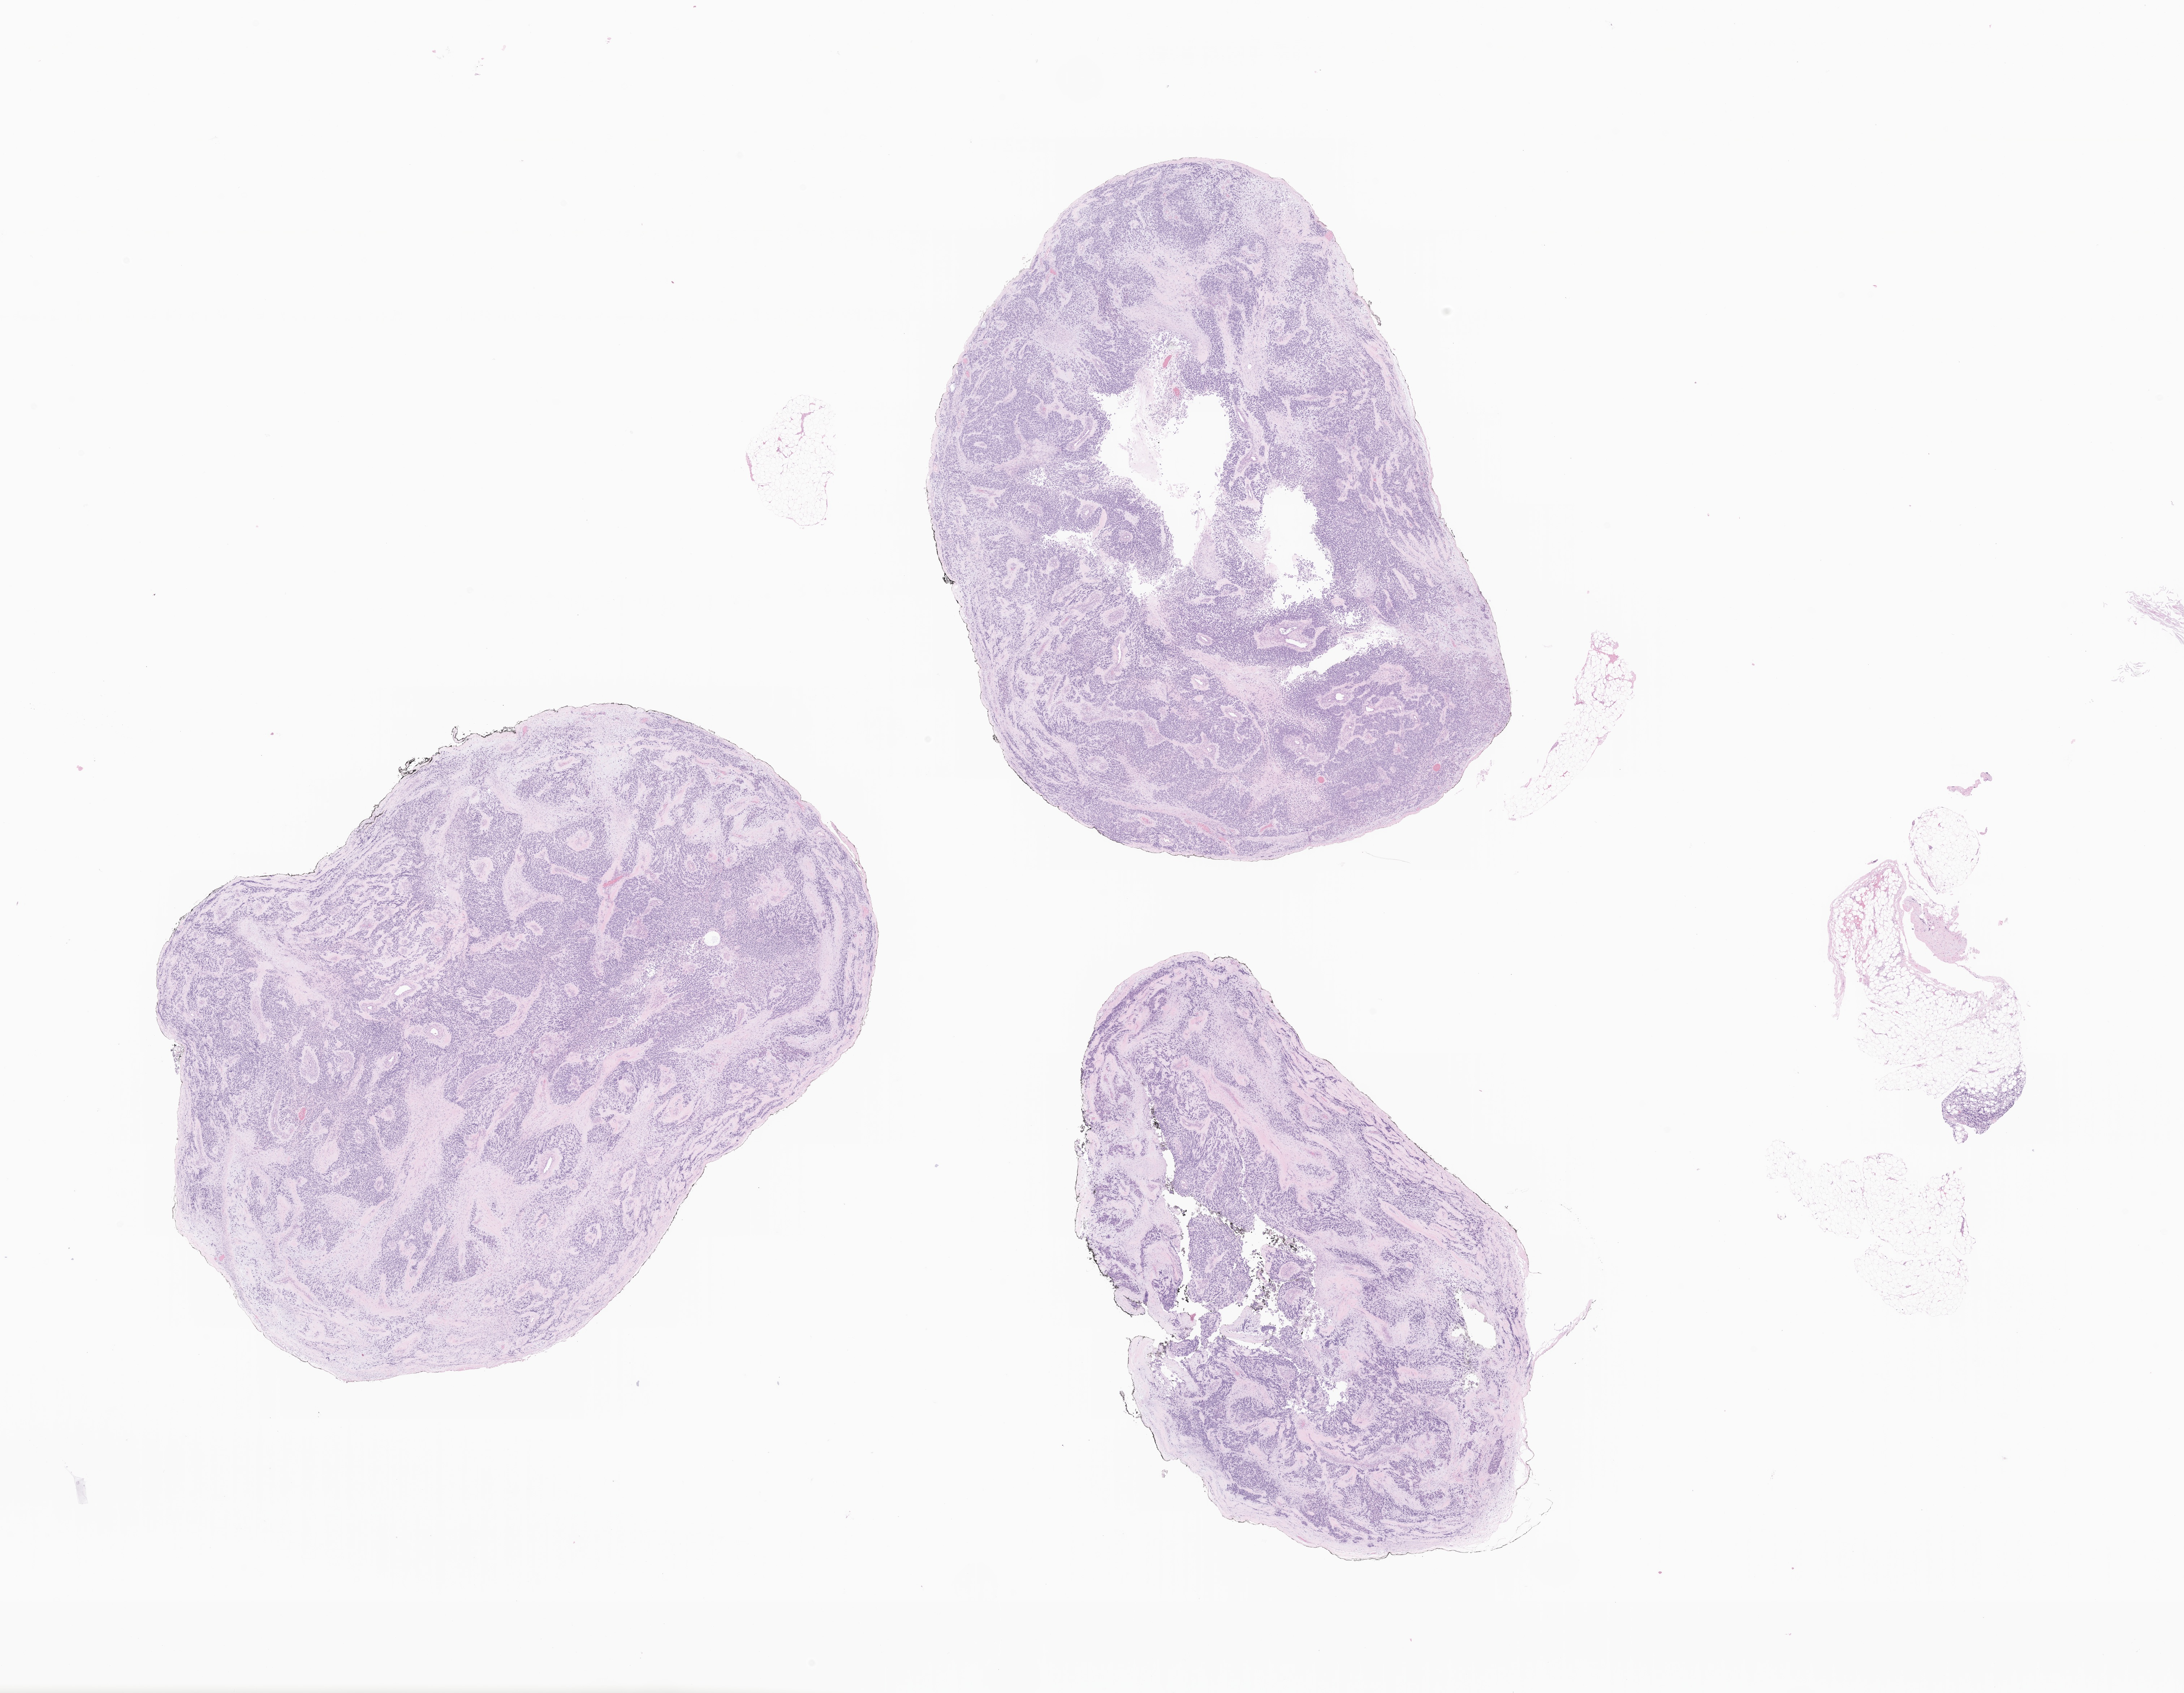
Digitized hematoxylin and eosin (H&E)-stained section of tumor tissue from the testis — low-resolution overview of the scanned area, about 25.5 x 19.8 mm, FFPE section. Male patient, age 181 months (15 years 1 month).
- diagnosis (ICD-O-3 morphology term): Rhabdomyosarcoma, NOS